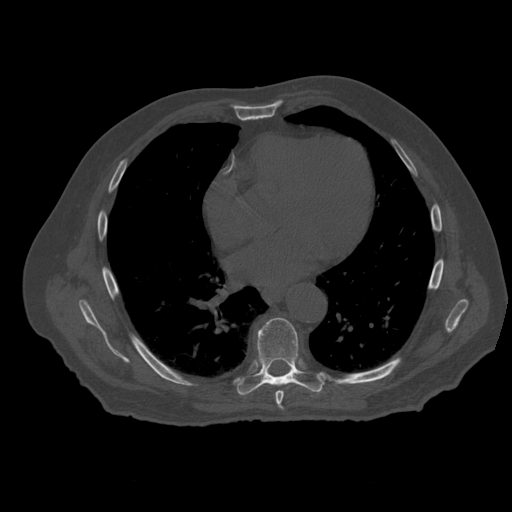
CT including the spine, one axial slice. Position 346 of 399 along the scan axis. Reconstruction kernel STANDARD. 120 kVp. Bone window (W 1800 / L 400 HU). 1.25 mm slice thickness. 512 × 512 image matrix, field of view 407 × 407 mm. Patient age 73 years. Case-level facts recorded for this patient, not image findings: primary cancer: prostate.
Annotated regions visible in this slice (semi-automatically segmented with operator editing):
- T7 vertebra: box from (x=276, y=391) to (x=284, y=410) px
- T8 vertebra: (x=237, y=318)–(x=325, y=396)